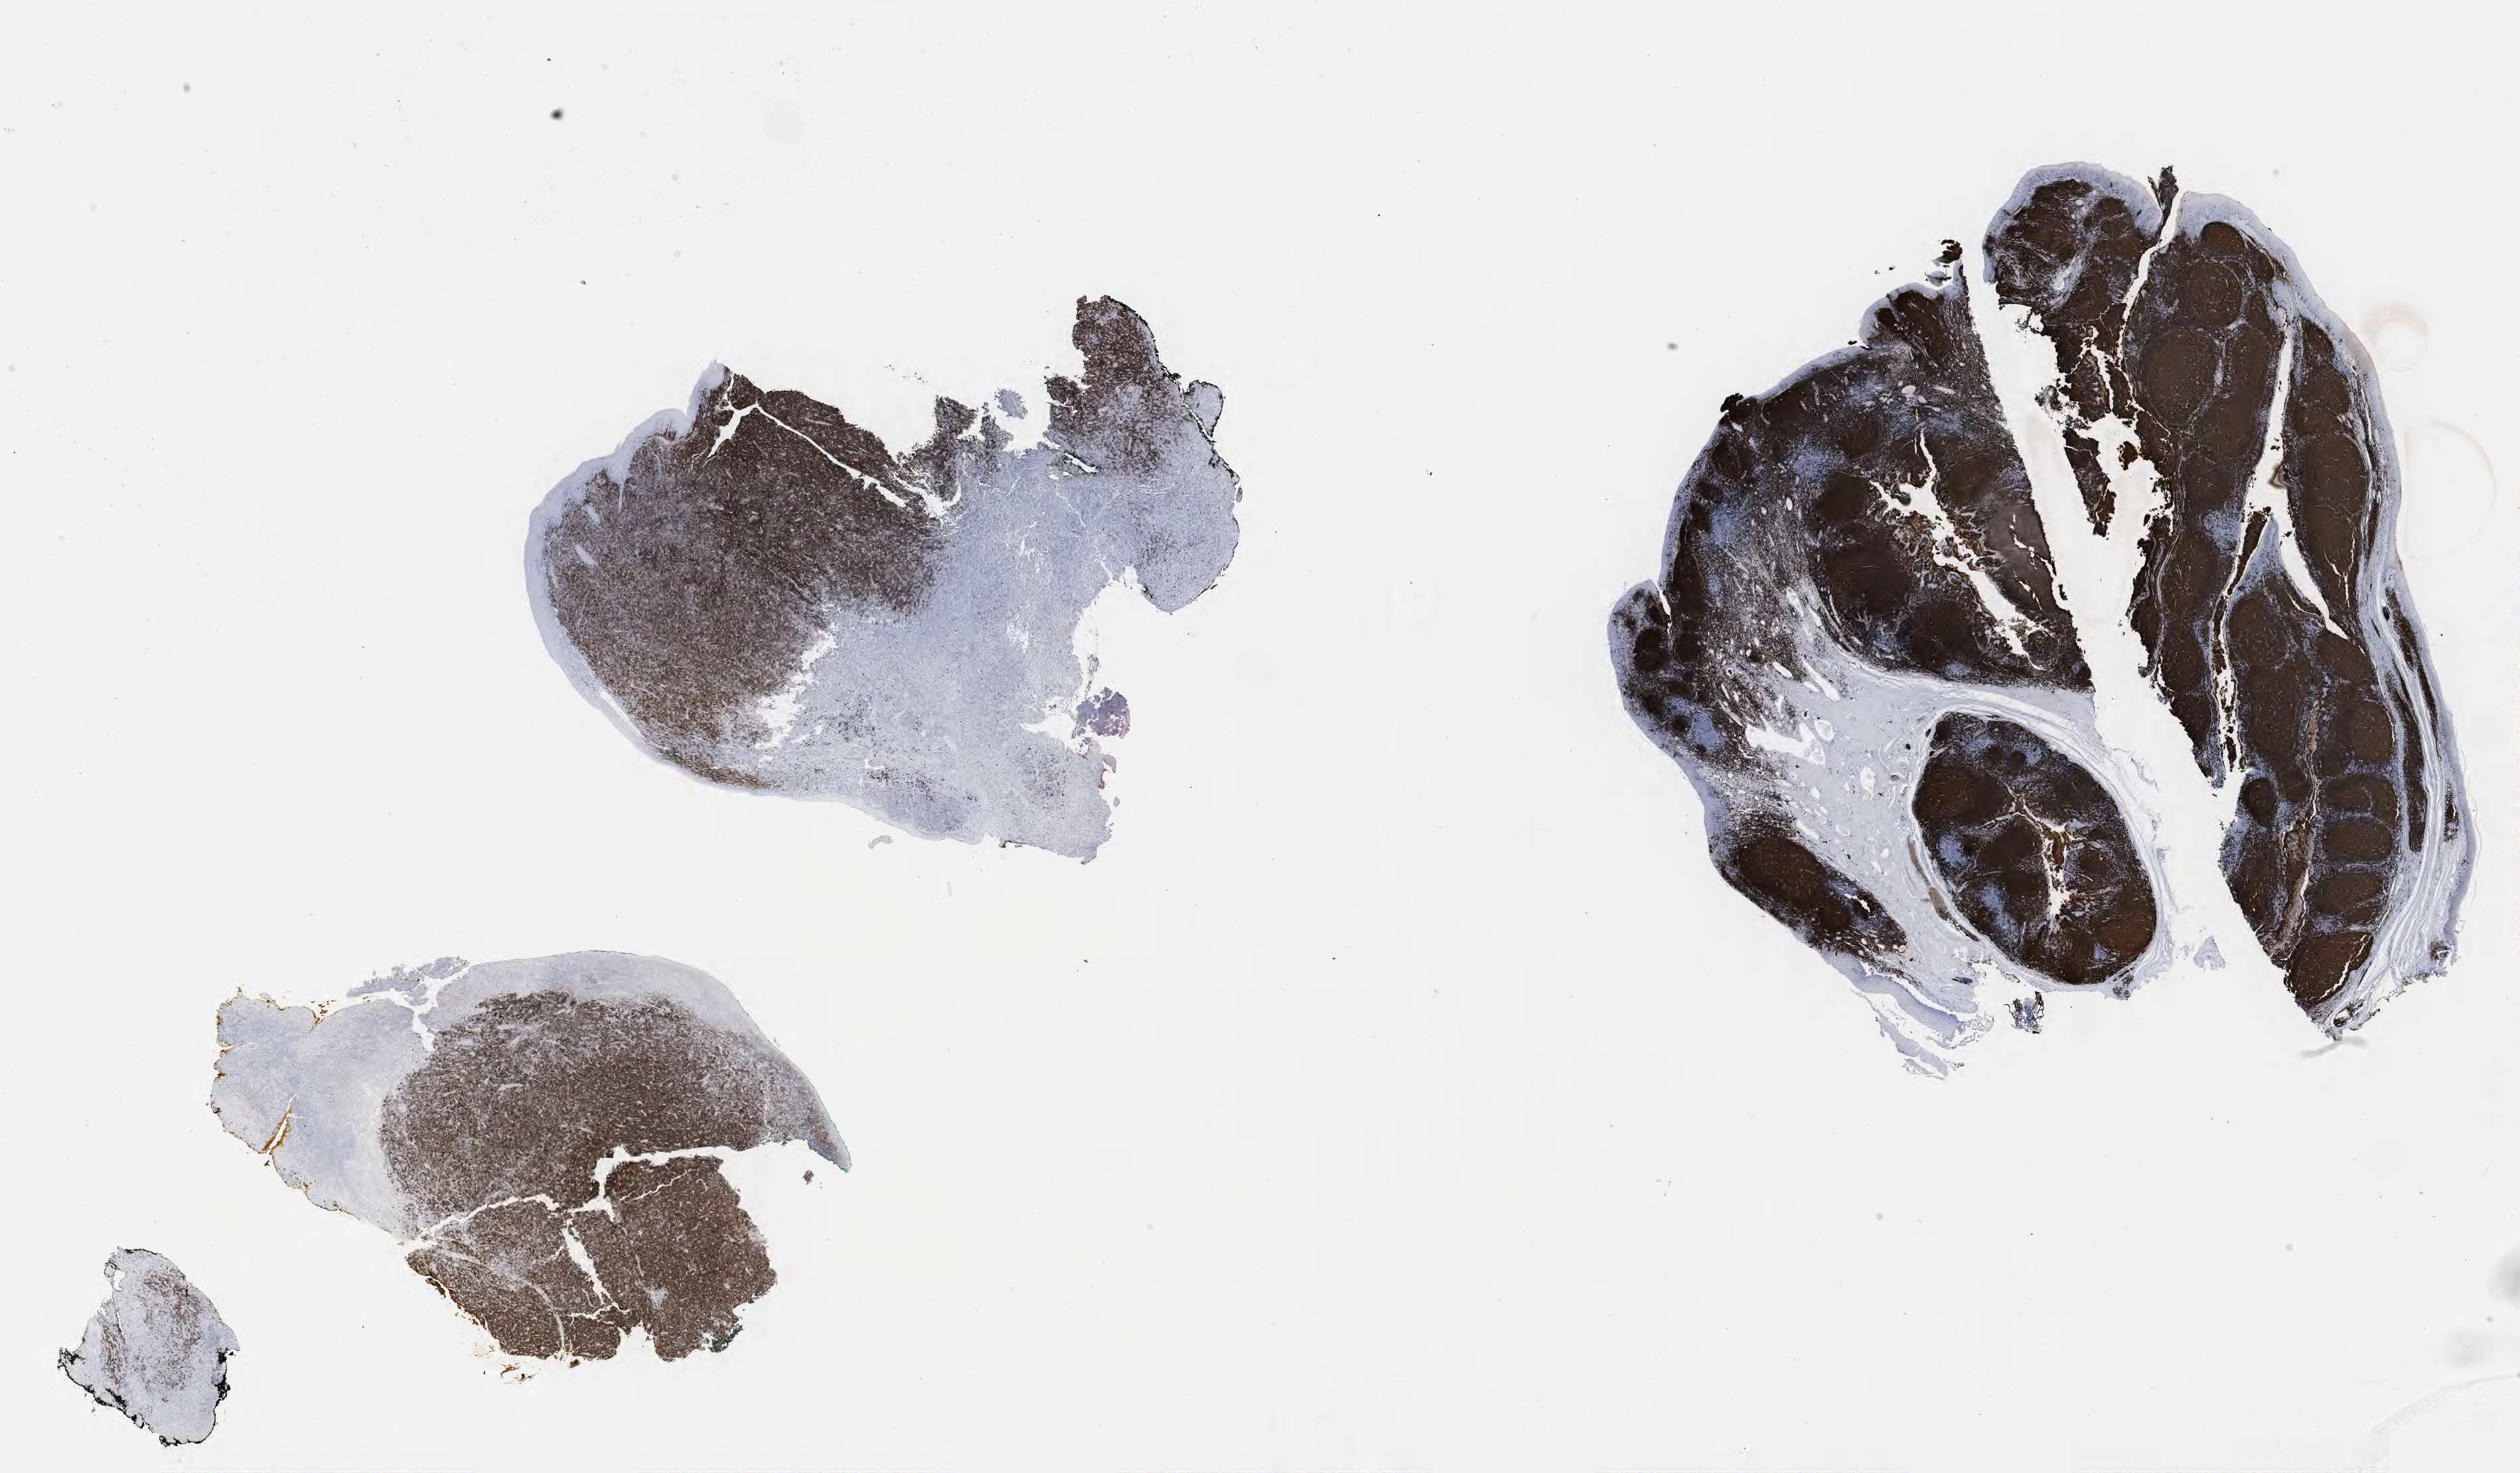
IHC for CD20, whole-slide image — low-resolution overview of the scanned area, about 30.7 x 17.9 mm, specimen: tumor tissue. Patient: male, aged 49.
Histologic diagnosis: Diffuse large B-cell lymphoma, NOS.